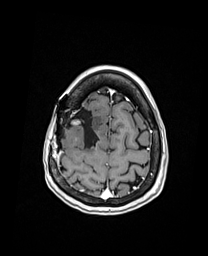
Brain MRI from a brain-tumour surgery series, one axial slice. Slice 39 of 192 in the series (ordered by position). T1-weighted post-contrast. 208 × 256 image matrix. Case-level facts recorded for this patient, not image findings: histopathology: Oligodendroglioma; WHO grade: 3; IDH mutation: yes; tumour location: Right Frontal.
Annotated regions visible in this slice (manually delineated by an expert):
- previous resection cavity: box from (x=72, y=109) to (x=99, y=148) px